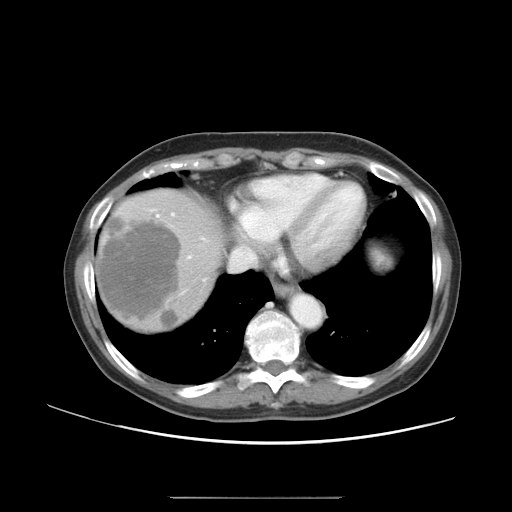
Contrast-enhanced abdominal CT, one axial slice. Reconstruction kernel STANDARD. 120 kVp. Intravenous contrast given. Soft-tissue window (W 400 / L 40 HU). 5 mm slice thickness. 512 × 512 image matrix. Female patient, age 58 years. From the clinical record (not read from this slice): diagnosis: colorectal cancer liver metastases, imaged before liver resection; multiple liver metastases: yes; largest metastasis: 7.3 cm; chemotherapy before resection: yes.
Outlined on this slice (expert manual segmentation):
- hepatic veins: bounding box [x1, y1, x2, y2] px = [171, 213, 267, 271]
- liver: [97, 191, 221, 331]
- planned liver remnant (the part of the liver to remain after resection): [202, 213, 217, 230]
- portal vein (with intrahepatic branches): [156, 214, 190, 258]
- liver metastasis: [162, 314, 182, 329]
- liver metastasis: [99, 218, 182, 328]